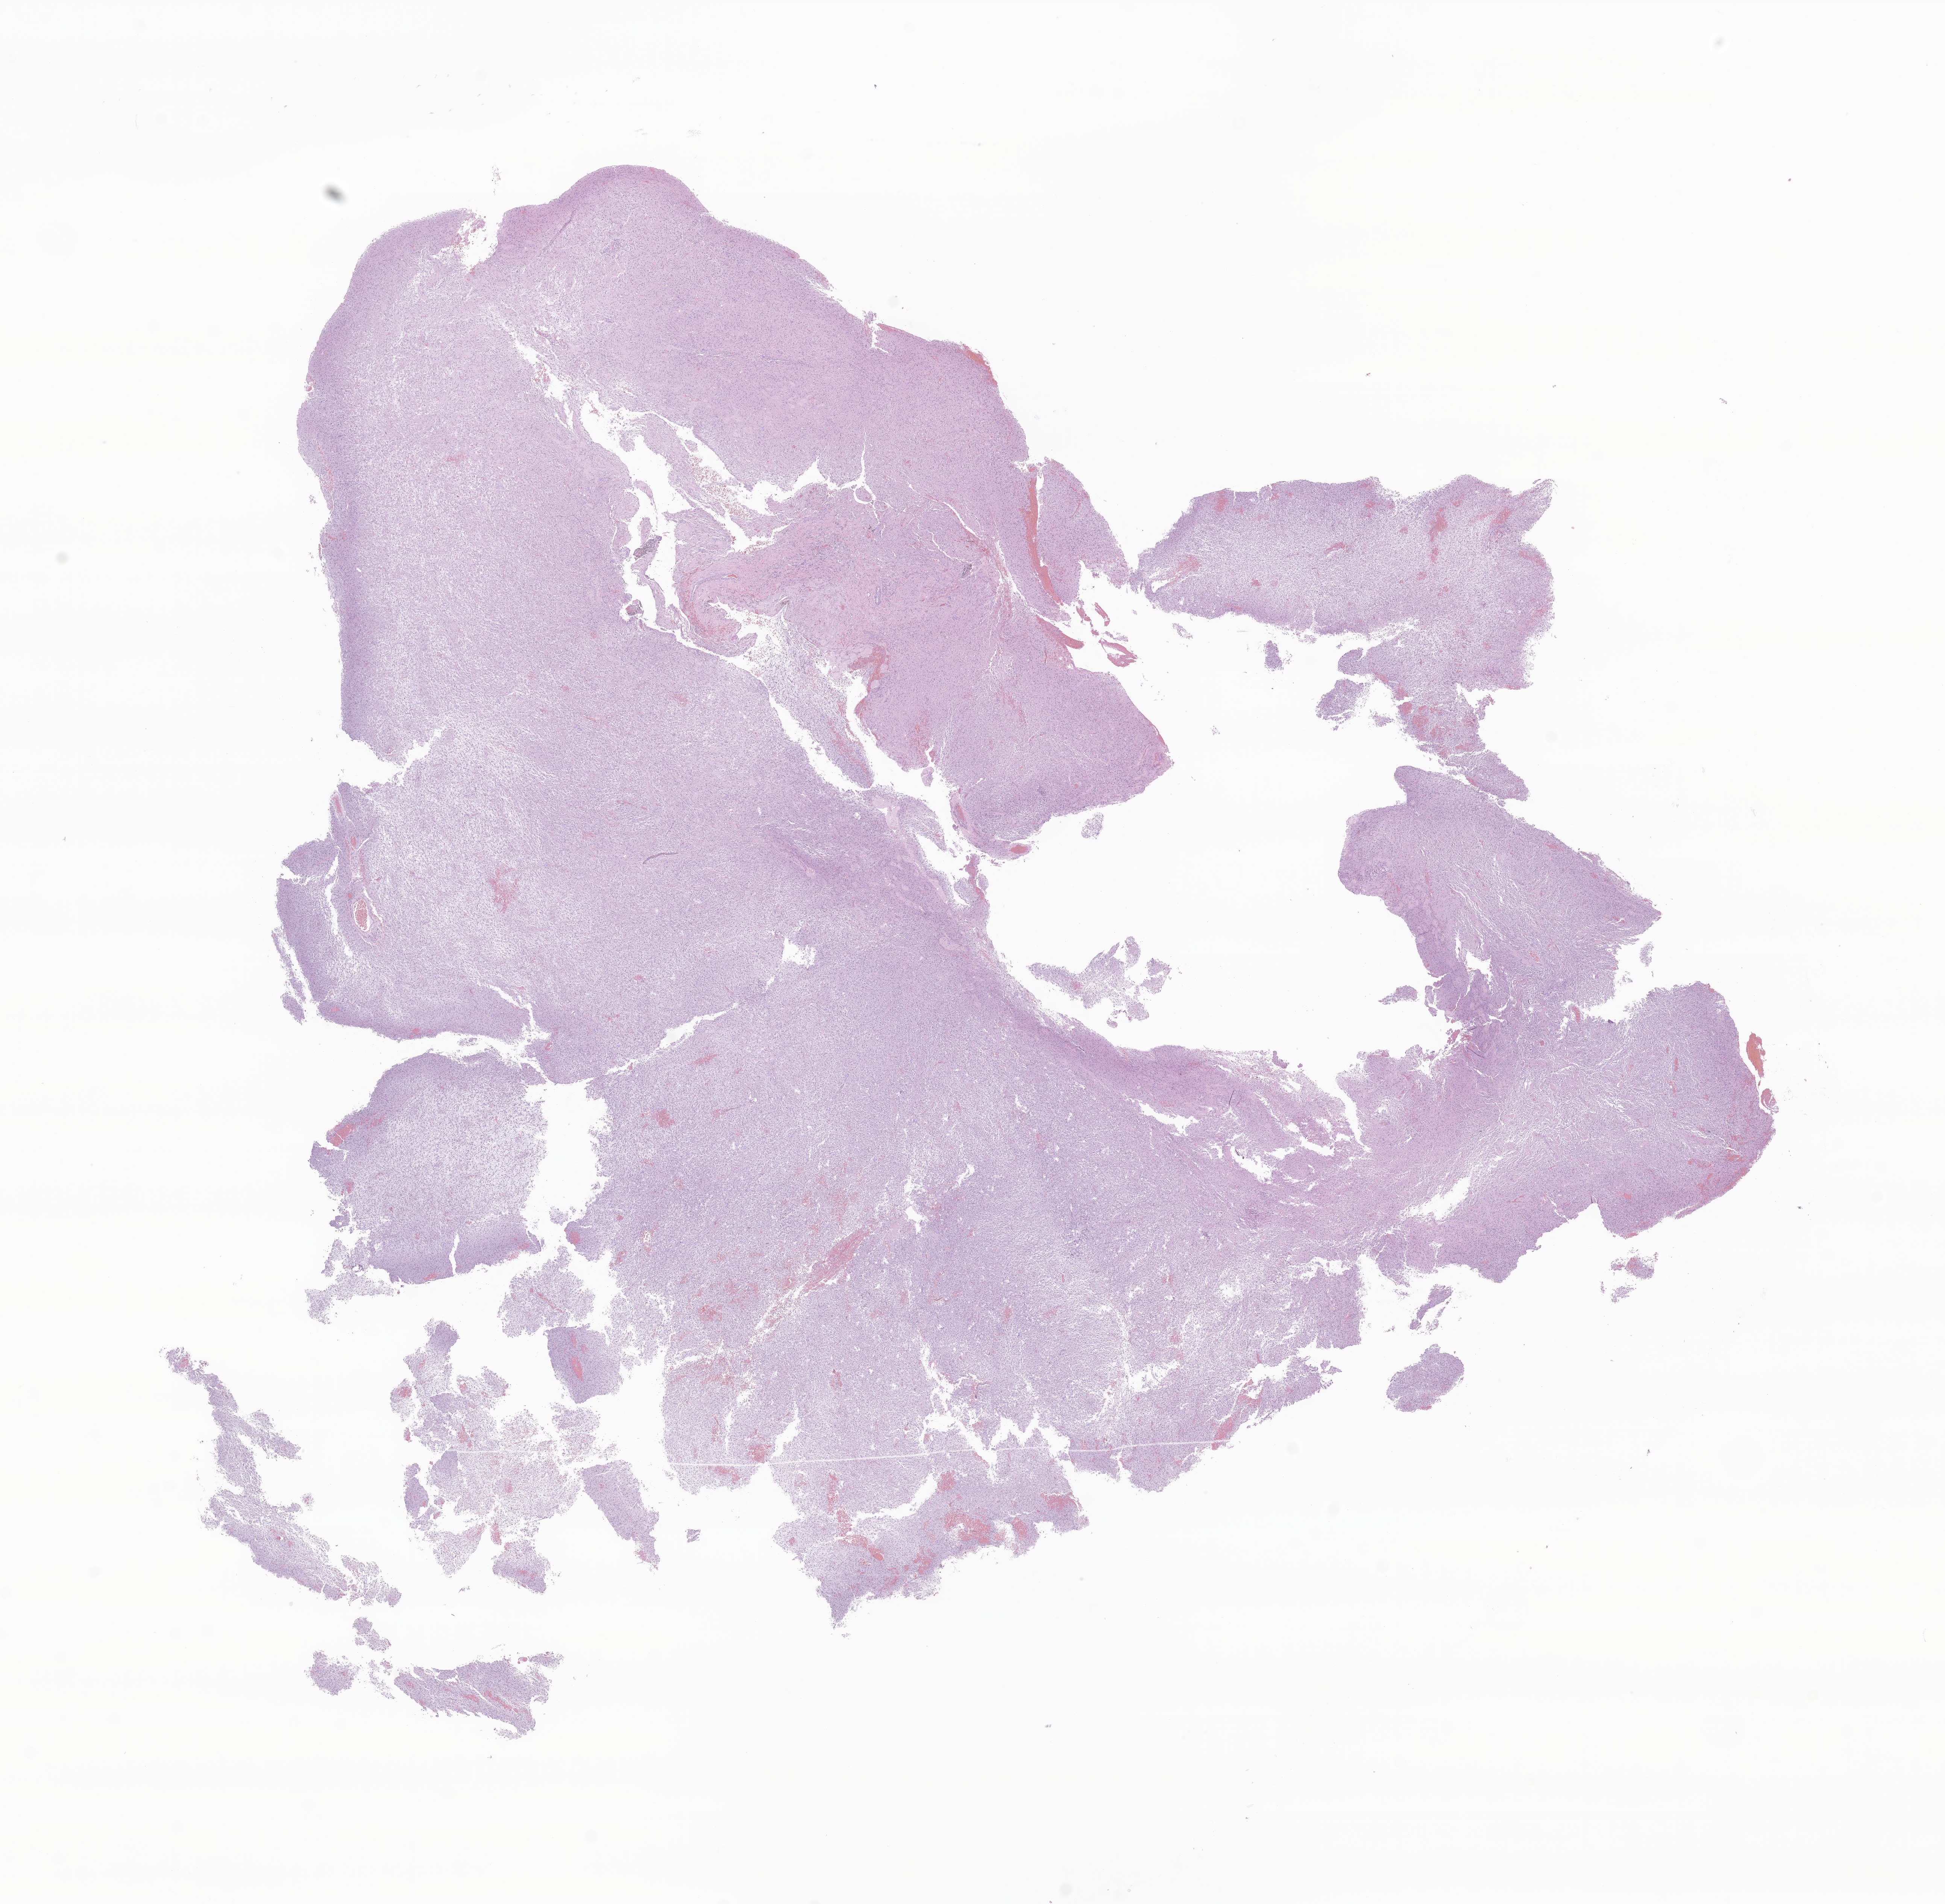
Hematoxylin and eosin (H&E) whole-slide image of tumor tissue from the brain, shown as a low-resolution overview of the whole scanned area (about 21.8 x 21.3 mm); formalin-fixed, paraffin-embedded (FFPE) tissue. Patient female; age 81 months (6 years 9 months).
Diagnosis (ICD-O-3 morphology term): Pilocytic astrocytoma.